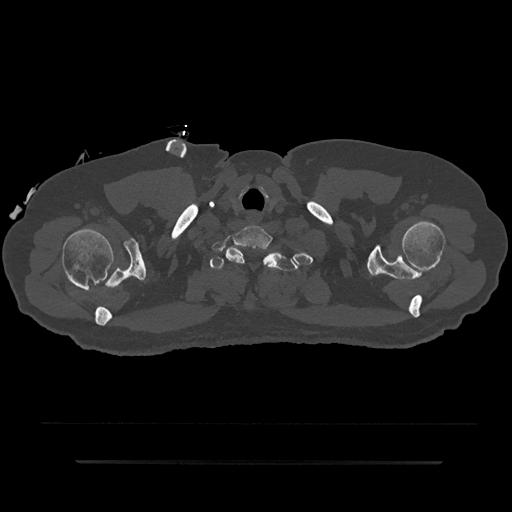
CT including the spine, one axial slice; slice 756 of 797 in the series (ordered by position); bone window (W 1800 / L 400 HU); 0.5 mm slice thickness; 512 × 512 image matrix. Male patient, age 59 years. Case-level facts recorded for this patient, not image findings: primary cancer: bile ducts; vertebrae with lytic lesions (as recorded): T10.
Outlined on this slice (semi-automatically segmented with operator editing):
- T1 vertebra: box from (x=210, y=249) to (x=298, y=271) px